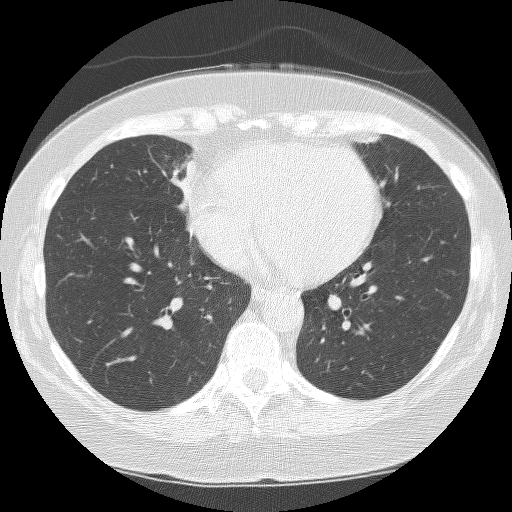
Low-dose screening chest CT, one axial slice. Position 70 of 159 along the scan axis. Reconstruction kernel BONE. 120 kVp. Lung window (W 1500 / L -600 HU). 512 × 512 image matrix, field of view 299 × 299 mm.
Structures marked on this image (outlined manually by an expert reader):
- lesion 1 (tumor, hilum of right lung): bounding box <171,161,195,206> (left, top, right, bottom; pixels)